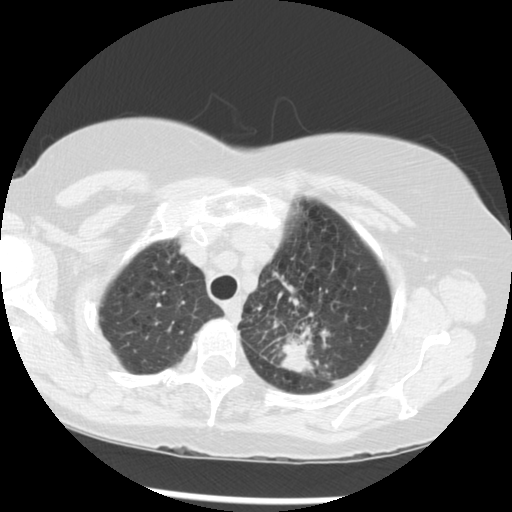
Axial slice from a low-dose chest CT screening exam; third screening round (two years after baseline); lung window (W 1500 / L -600 HU); 2.5 mm slice thickness; 120 kVp. Female participant, aged 70 years at enrolment. Current smoker at enrolment.
Expert-annotated lung lesion, bounding box <251,286,349,374> (left, top, right, bottom; pixels). The exam's reader record, not a measurement of the box and not confirmed to be the same lesion: non-calcified nodule or mass ≥4 mm, left upper lobe, 32 × 26 mm, spiculated (stellate) margins, soft tissue attenuation, pre-existing on the prior screen: yes; interval growth: yes. Official screen result: positive, other. Participant outcome: lung cancer diagnosed 24 days after this screen — neoplasm, malignant, left upper lobe, stage IIIB (AJCC 6th edition), 40 mm at pathology.